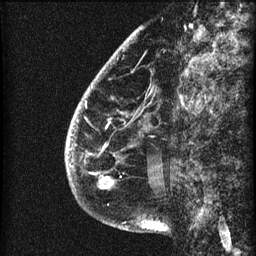
Breast MRI (dynamic contrast-enhanced), one sagittal slice; slice 15 of 60 in the series (ordered by position); 3 images stored at this slice position (order not interpretable as contrast timing); 1.5 T; TE 4.2 ms, TR 22.7 ms; 2 mm slice thickness; 256 × 256 image matrix, field of view 180 × 180 mm. Patient: female, 48 years. From the clinical record (not read from this slice): setting: breast cancer imaged before/during neoadjuvant chemotherapy; receptor status: triple-negative.
Annotated regions visible in this slice (semi-automatic segmentation, software-assisted and operator-edited):
- analysis volume of interest (the breast-tissue region the enhancement analysis was run in; not a lesion): bounding box <66,30,173,207> (left, top, right, bottom; pixels)
- tumour enhancement mask (voxels above the 90 % enhancement threshold inside the analysis volume of interest): <68,138,113,188>